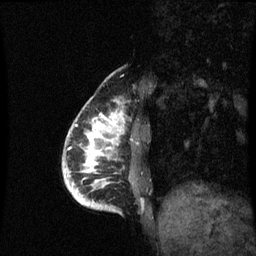
Breast MRI (dynamic contrast-enhanced), one sagittal slice. Position 17 of 60 along the scan axis. Dynamic contrast-enhanced series, image 2 of 3 at this slice position (ordered by acquisition). 1.5 T. TE 4.2 ms, TR 8.9 ms. 256 × 256 image matrix. Patient: female, 35 years. From the clinical record (not read from this slice): setting: breast cancer imaged before/during neoadjuvant chemotherapy; receptor status: HR-positive, HER2-negative.
Annotated regions visible in this slice (semi-automatic segmentation, software-assisted and operator-edited):
- analysis volume of interest (the breast-tissue region the enhancement analysis was run in; not a lesion): box from (x=66, y=106) to (x=131, y=209) px
- tumour enhancement mask (voxels above the 70 % enhancement threshold inside the analysis volume of interest): (x=80, y=118)–(x=119, y=205)